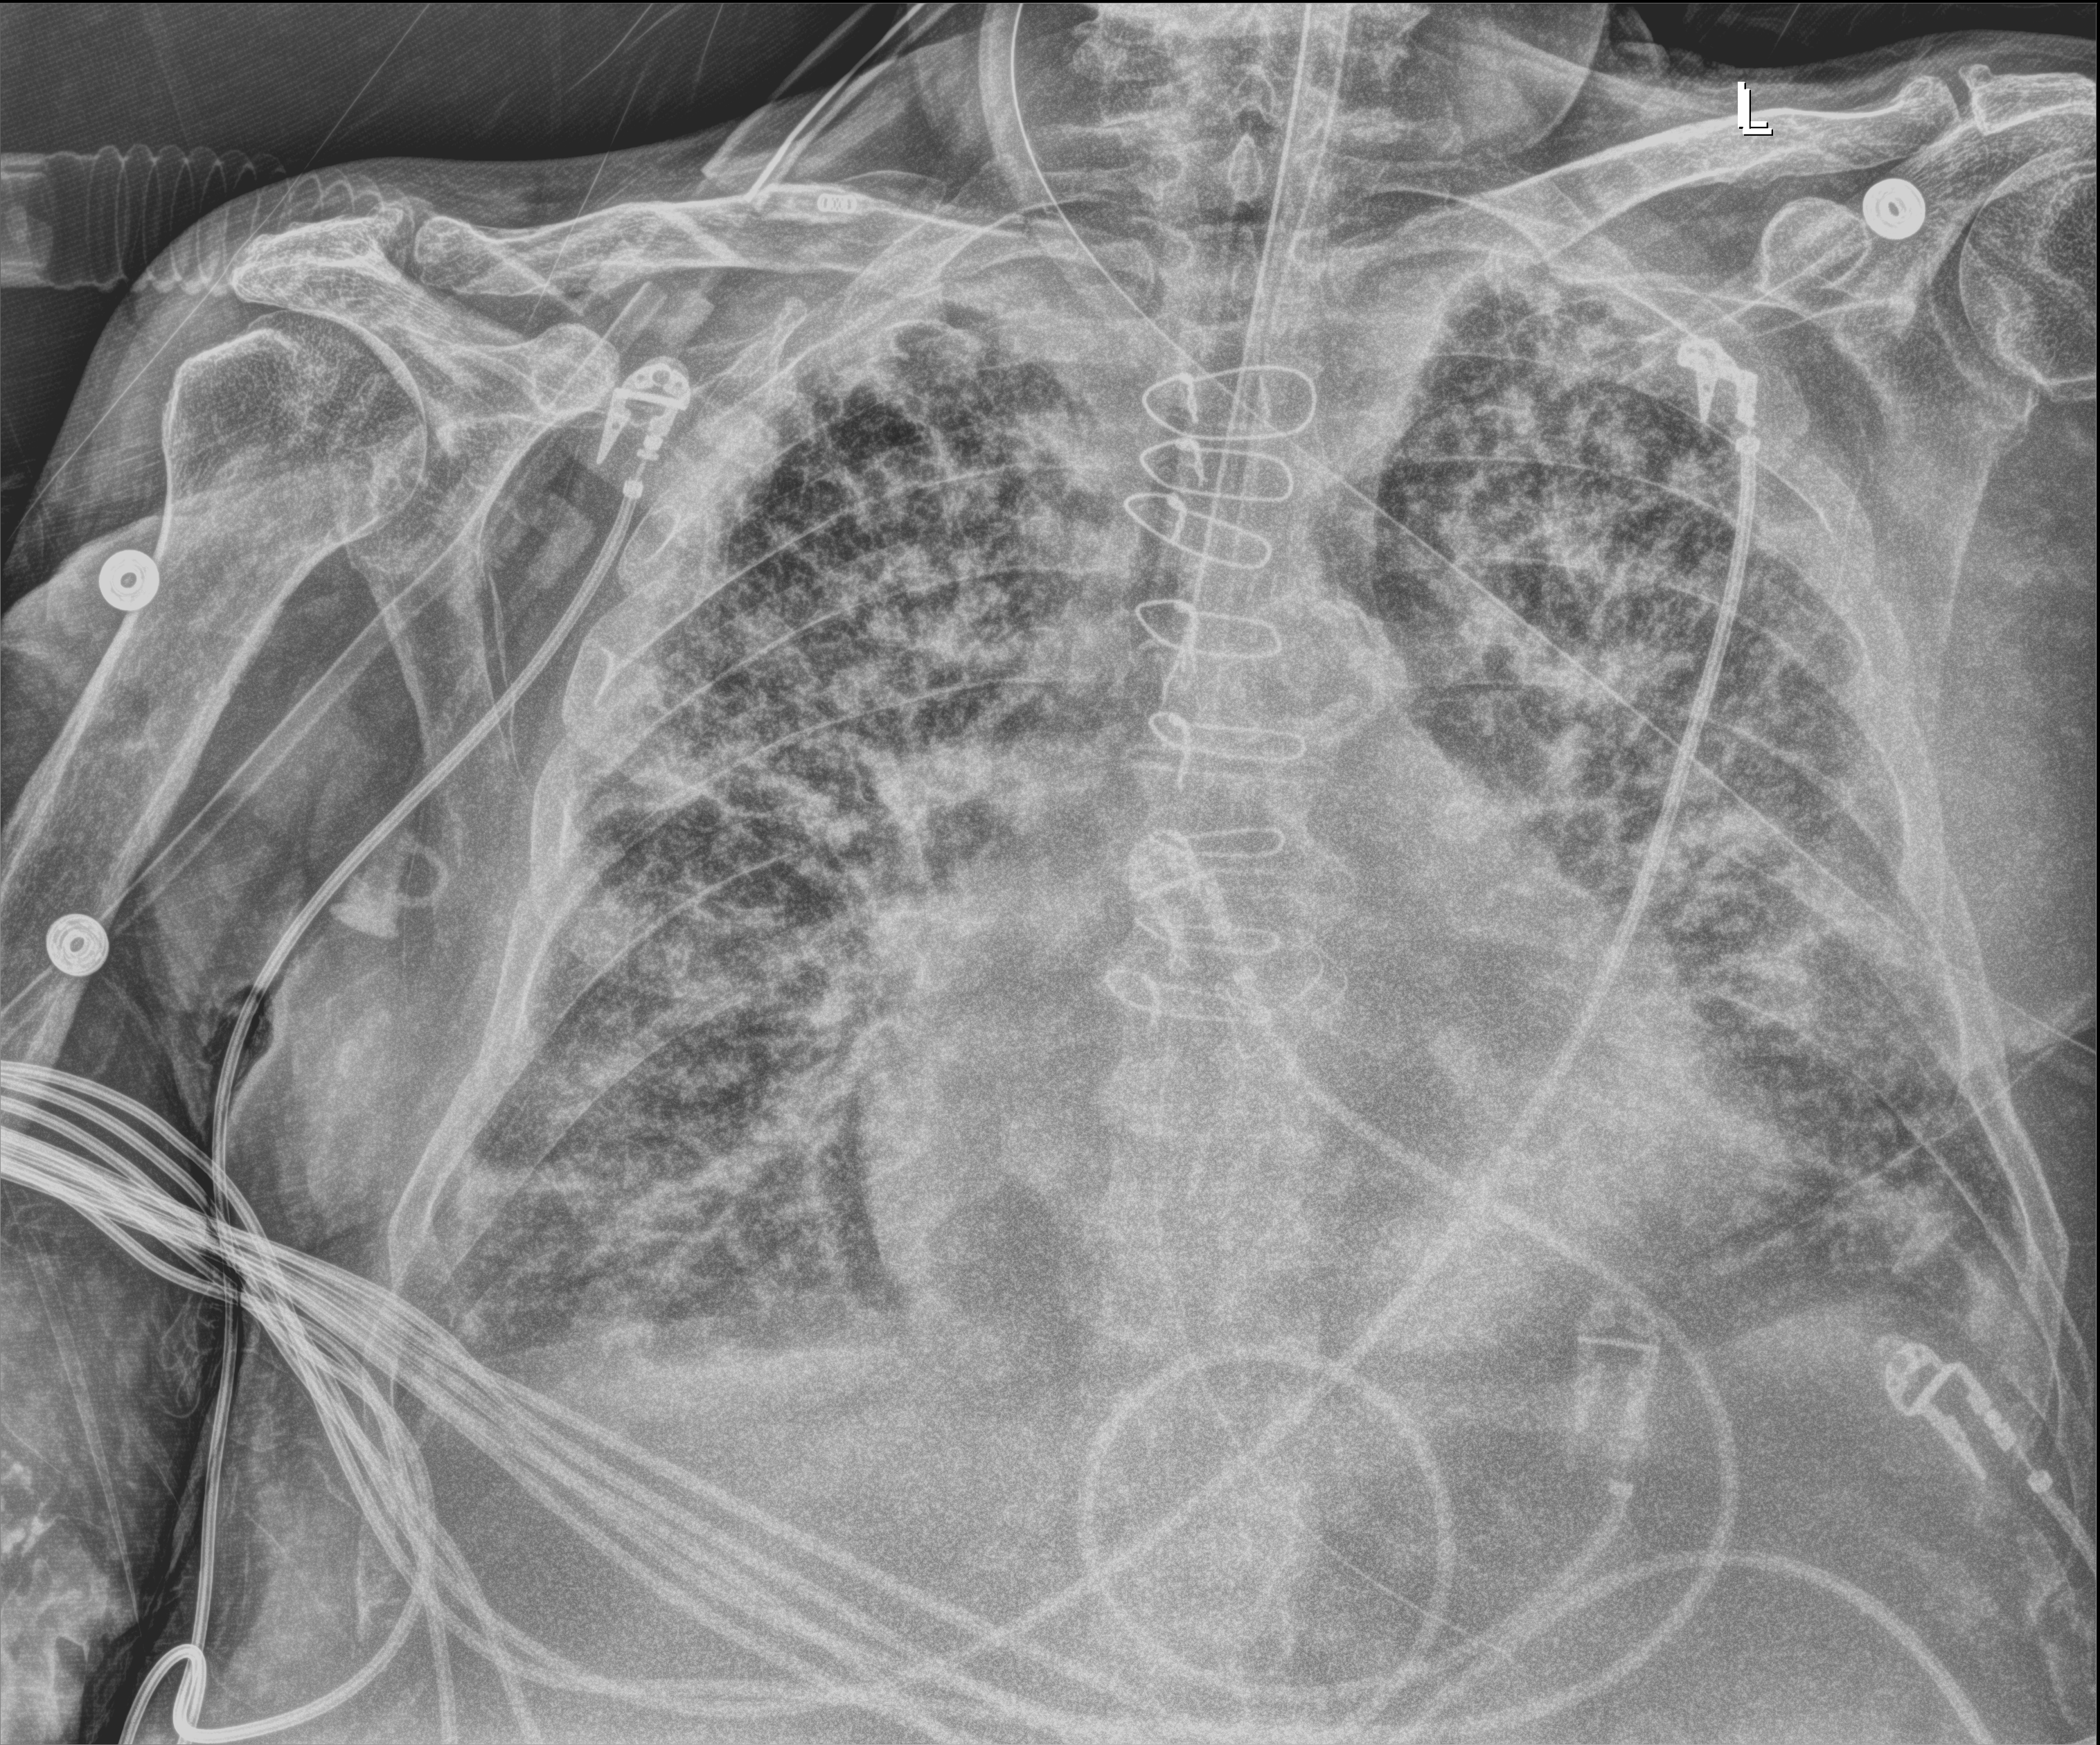
Bedside chest radiograph (digital radiography), anteroposterior (AP) projection. Patient hospitalised with COVID-19; male, aged 75–90 years.
From the hospital-stay record, not from the radiograph (when in the stay this image was taken is not recorded): admitted to intensive care during this hospital stay: yes; mechanically ventilated during this hospital stay: yes.